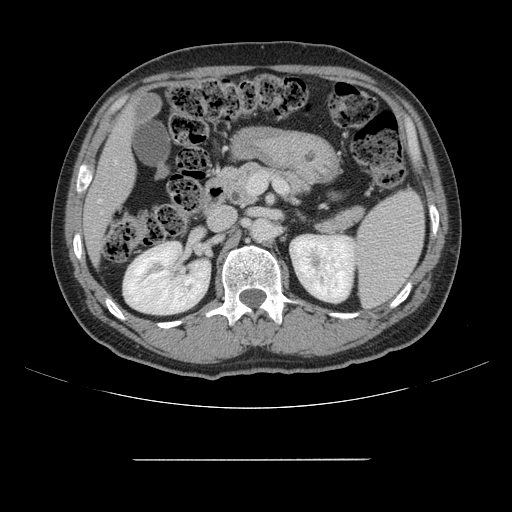
Contrast-enhanced abdominal CT, one axial slice; position 70 of 164 along the scan axis; 120 kVp; intravenous contrast given; soft-tissue window (W 400 / L 40 HU); 2.5 mm slice thickness; 512 × 512 image matrix, field of view 404 × 404 mm. Male patient, age 54 years. Case-level facts recorded for this patient, not image findings: diagnosis: colorectal cancer liver metastases, imaged before liver resection.
Annotated regions visible in this slice (manually delineated by an expert):
- hepatic veins: bounding box (x1, y1, x2, y2) in pixels: (98, 161, 117, 202)
- liver: (85, 111, 135, 259)
- planned liver remnant (the part of the liver to remain after resection): (85, 110, 135, 259)